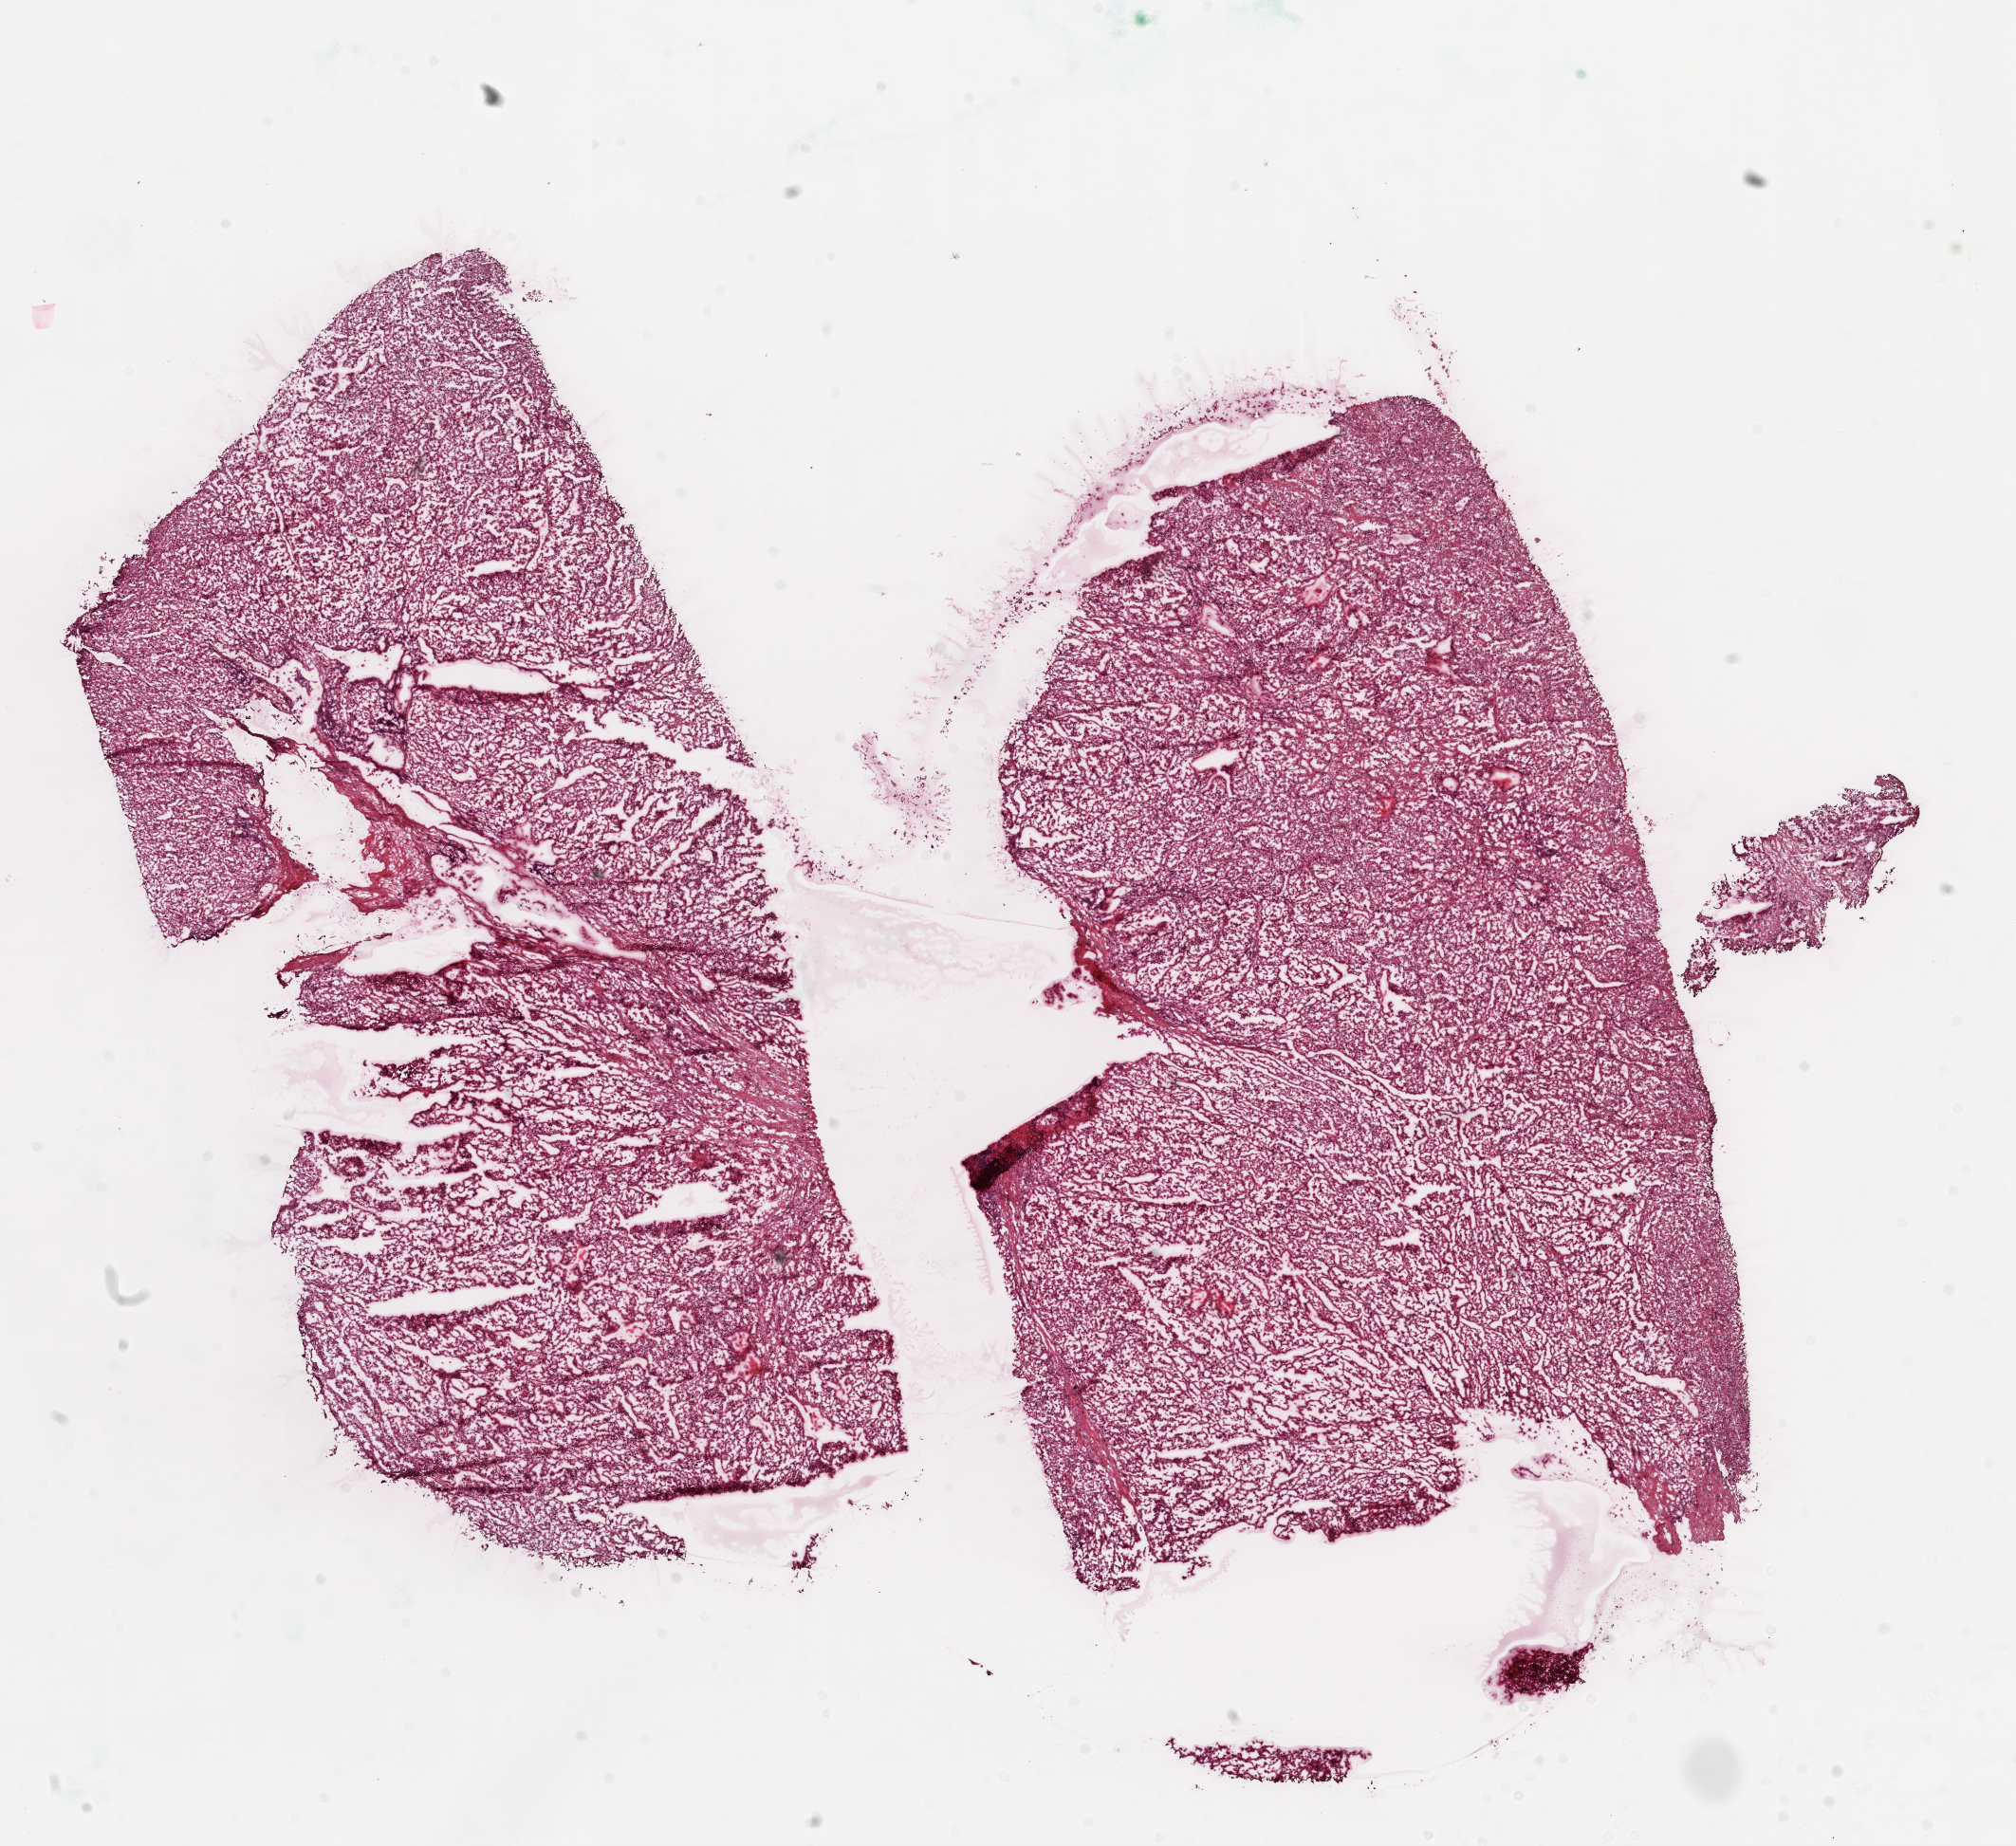
Digitized H&E-stained tissue section (whole slide) — shown as a low-resolution overview of the whole scanned area (about 17.1 x 15.6 mm, from a 20x scan), frozen section, primary tumour sample from the kidney. Patient: male, age at initial diagnosis 57 years. Histologic grade: G4 (undifferentiated). Pathologist review of this section (percent, as recorded): tumour cells 100%, tumour nuclei 85%, necrosis 0%.
AJCC pathologic stage: III. Lymph nodes positive (case pathology): 2 of 16 examined. Pathologic diagnosis: Clear cell adenocarcinoma, NOS.